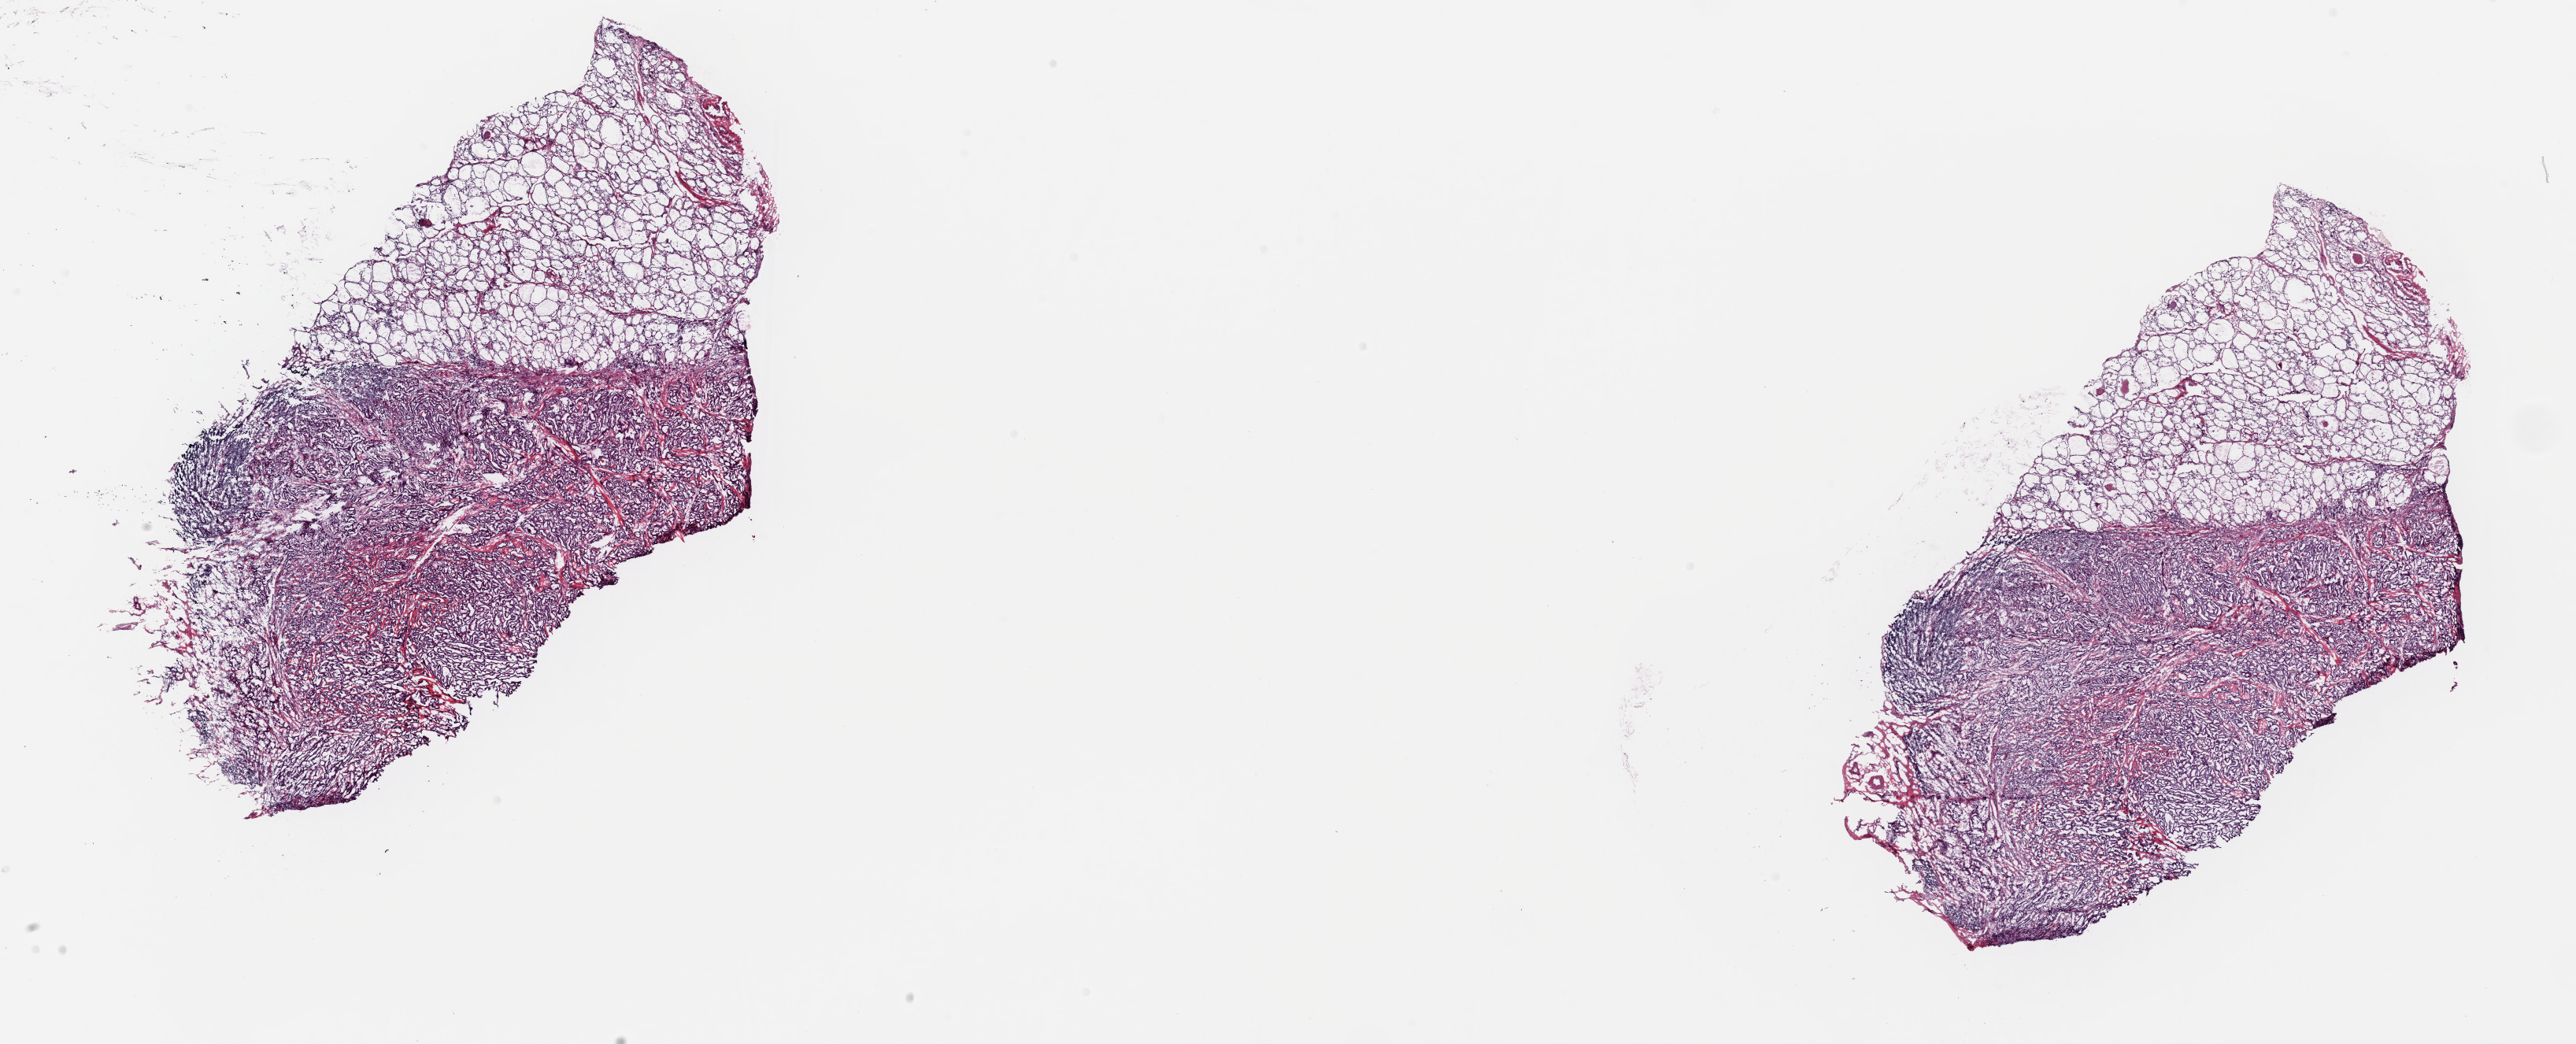
H&E whole-slide image — shown as a low-resolution overview of the whole scanned area (about 25.8 x 10.5 mm), frozen section, thyroid, primary tumour sample. Female, age 70 years at initial diagnosis. Composition of this section per pathologist review: tumour cells 85%, tumour nuclei 85%, normal cells 0%, stromal cells 15%, necrosis 0%. Inflammatory infiltration, as recorded: lymphocyte infiltration 0%, monocyte infiltration 0%, neutrophil infiltration 0%.
TNM: T1 N1a M0. Pathologic diagnosis: Papillary adenocarcinoma, NOS (thyroid gland). AJCC pathologic stage: III.